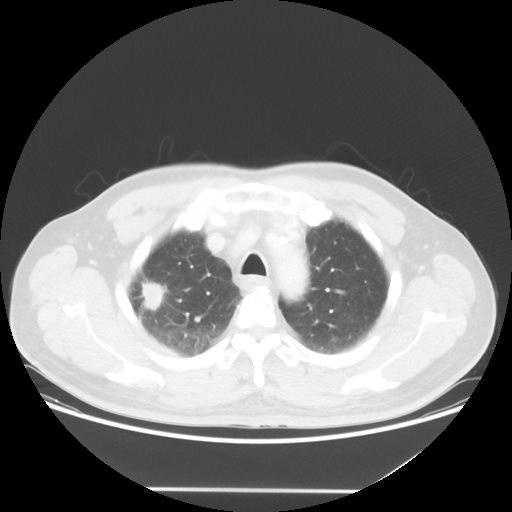
Chest CT, one axial slice; slice 43 of 54 in the series (ordered by position); lung window (W 1500 / L -600 HU); 5 mm slice thickness; 512 × 512 image matrix, field of view 416 × 416 mm. Male patient, age 65 years. From the clinical record (not read from this slice): clinical TNM (as recorded): T1c N1 M0.
Structures marked on this image (bounding box drawn by a radiologist):
- lung tumour (recorded histology: adenocarcinoma): bounding box <134,276,170,319> (left, top, right, bottom; pixels)